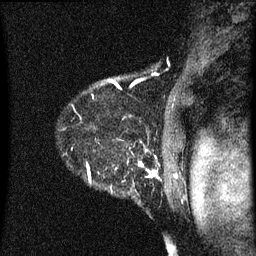
Breast MRI (dynamic contrast-enhanced), one sagittal slice. Position 54 of 60 along the scan axis. Dynamic contrast-enhanced series, image 2 of 3 at this slice position (ordered by acquisition). 1.5 T. TE 4.2 ms, TR 8 ms. 2 mm slice thickness. 256 × 256 image matrix. Female patient, age 54 years.
Annotated regions visible in this slice (semi-automatic segmentation, software-assisted and operator-edited):
- analysis volume of interest (the breast-tissue region the enhancement analysis was run in; not a lesion): bounding box [x1, y1, x2, y2] px = [57, 138, 164, 209]
- tumour enhancement mask (voxels above the 70 % enhancement threshold inside the analysis volume of interest): [72, 150, 159, 183]